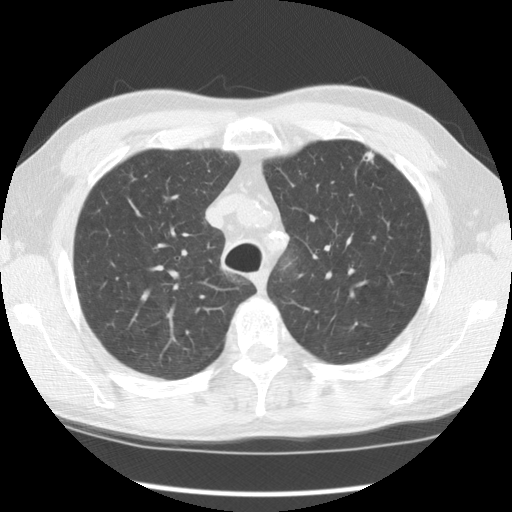
Low-dose screening chest CT, one axial slice; slice 93 of 121 in the series (ordered by position); reconstruction kernel STANDARD; lung window (W 1500 / L -600 HU); 512 × 512 image matrix, field of view 350 × 350 mm.
Annotated regions visible in this slice (manually delineated by an expert):
- lesion 1 (tumor, upper lobe of left lung): bounding box <363,150,375,162> (left, top, right, bottom; pixels)